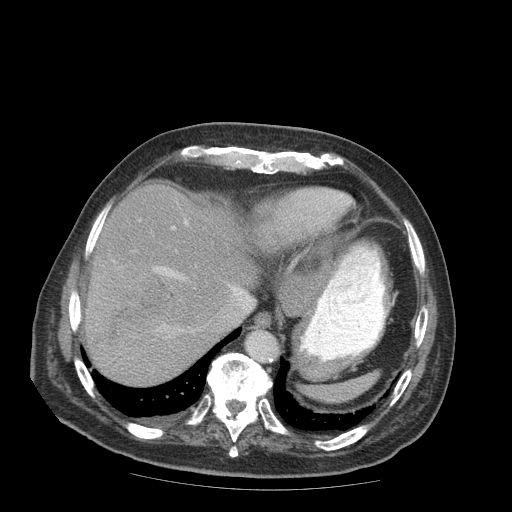
Contrast-enhanced abdominal CT (liver protocol), one axial slice. Slice 72 of 99 in the series (ordered by position). Reconstruction kernel STANDARD. Soft-tissue window (W 400 / L 40 HU). 2.5 mm slice thickness. 512 × 512 image matrix. Case-level facts recorded for this patient, not image findings: diagnosis: hepatocellular carcinoma (patient treated with transarterial chemoembolisation; whether this scan precedes or follows treatment is not stated here); TNM stage (as recorded): Stage-IIIB.
Structures marked on this image (semi-automatic segmentation, software-assisted and operator-edited):
- liver parenchyma outside the tumour (the mass and vessels are separate outlines, so this box may not span the whole liver): bounding box <86,184,256,384> (left, top, right, bottom; pixels)
- mass: <97,257,177,338>
- liver vessels: <153,220,240,332>